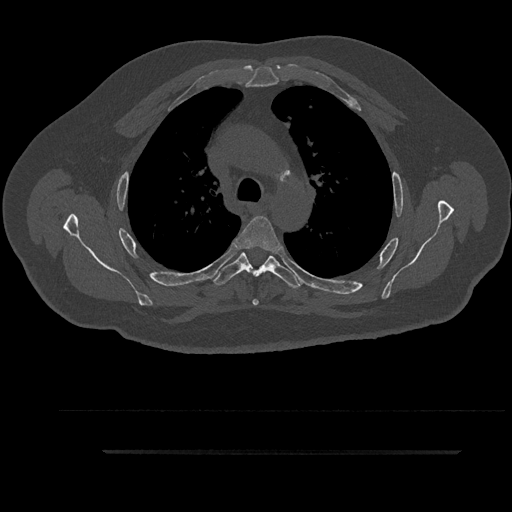
CT including the spine, one axial slice; slice 650 of 797 in the series (ordered by position); reconstruction kernel Br40s/3; bone window (W 1800 / L 400 HU); 512 × 512 image matrix, field of view 432 × 432 mm. Male patient, age 63 years. From the clinical record (not read from this slice): primary cancer: renal; vertebrae with lytic lesions (as recorded): T8.
Structures marked on this image (semi-automatic segmentation, software-assisted and operator-edited):
- T3 vertebra: bounding box (x1, y1, x2, y2) in pixels: (213, 258, 288, 282)
- T4 vertebra: (236, 216, 281, 306)
- T5 vertebra: (214, 252, 300, 290)